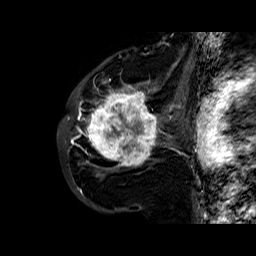
Breast MRI (dynamic contrast-enhanced), one sagittal slice. Slice 37 of 60 in the series (ordered by position). Dynamic contrast-enhanced series, time point 2 of 6 at this slice position (early post-contrast). 1.5 T. TE 6.4 ms, TR 32.8 ms. 256 × 256 image matrix, field of view 200 × 200 mm. Female patient. From the clinical record (not read from this slice): setting: breast cancer imaged before/during neoadjuvant chemotherapy; receptor status: HR-positive, HER2-negative.
Structures marked on this image (semi-automatically segmented with operator editing):
- analysis volume of interest (the breast-tissue region the enhancement analysis was run in; not a lesion): bounding box [x1, y1, x2, y2] px = [86, 77, 163, 177]
- tumour enhancement mask (voxels above the 100 % enhancement threshold inside the analysis volume of interest): [86, 81, 159, 167]